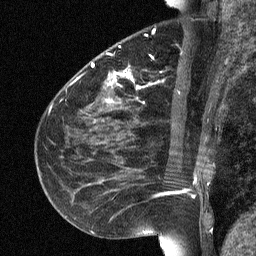
Breast MRI (dynamic contrast-enhanced), one sagittal slice. Position 26 of 64 along the scan axis. Dynamic contrast-enhanced study with each time point stored as its own series, time point 2 of 3 at this slice position (early post-contrast, ordered by acquisition time). 1.5 T. TE 4.8 ms, TR 27 ms. 256 × 256 image matrix, field of view 180 × 180 mm. Female patient, age 51 years. Case-level facts recorded for this patient, not image findings: setting: breast cancer imaged before/during neoadjuvant chemotherapy; receptor status: HR-positive, HER2-negative.
Annotated regions visible in this slice (semi-automatically segmented with operator editing):
- analysis volume of interest (the breast-tissue region the enhancement analysis was run in; not a lesion): bounding box <72,34,182,118> (left, top, right, bottom; pixels)
- tumour enhancement mask (voxels above the 90 % enhancement threshold inside the analysis volume of interest): <92,63,133,102>